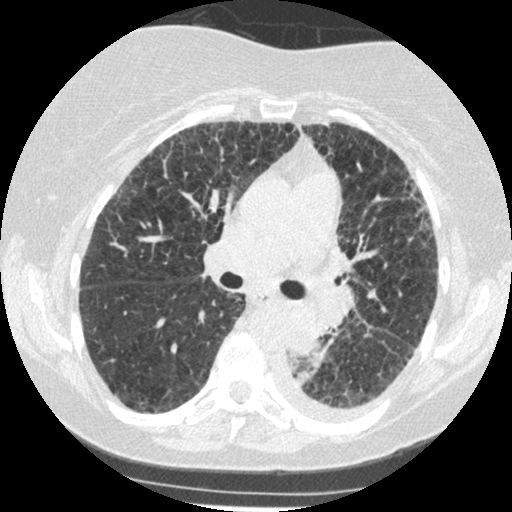
Low-dose screening chest CT, axial slice, third screening round (two years after baseline), lung window (W 1500 / L -600 HU), 1.25 mm slice thickness, standard (soft-tissue) reconstruction kernel (STANDARD), slice 186 of 341 in the series, 512 × 512 image matrix, field of view 310 × 310 mm. Female participant, aged 60 years at enrolment. Former smoker at enrolment.
• Lesion marked by an expert reader, bounding box [x1, y1, x2, y2] px = [269, 308, 342, 373].
• Reader record for this screening exam (exam-level; its link to the box is not recorded): non-calcified nodule or mass ≥4 mm, left lower lobe, 54 × 38 mm, smooth margins, soft tissue attenuation, pre-existing on the prior screen: yes; interval growth: yes.
• Official screen result: positive, other.
• Later outcome: lung cancer diagnosed 15 days after this screen — small cell carcinoma, NOS, left lower lobe, undifferentiated (G4), stage IV (AJCC 6th edition), 69 mm at pathology.